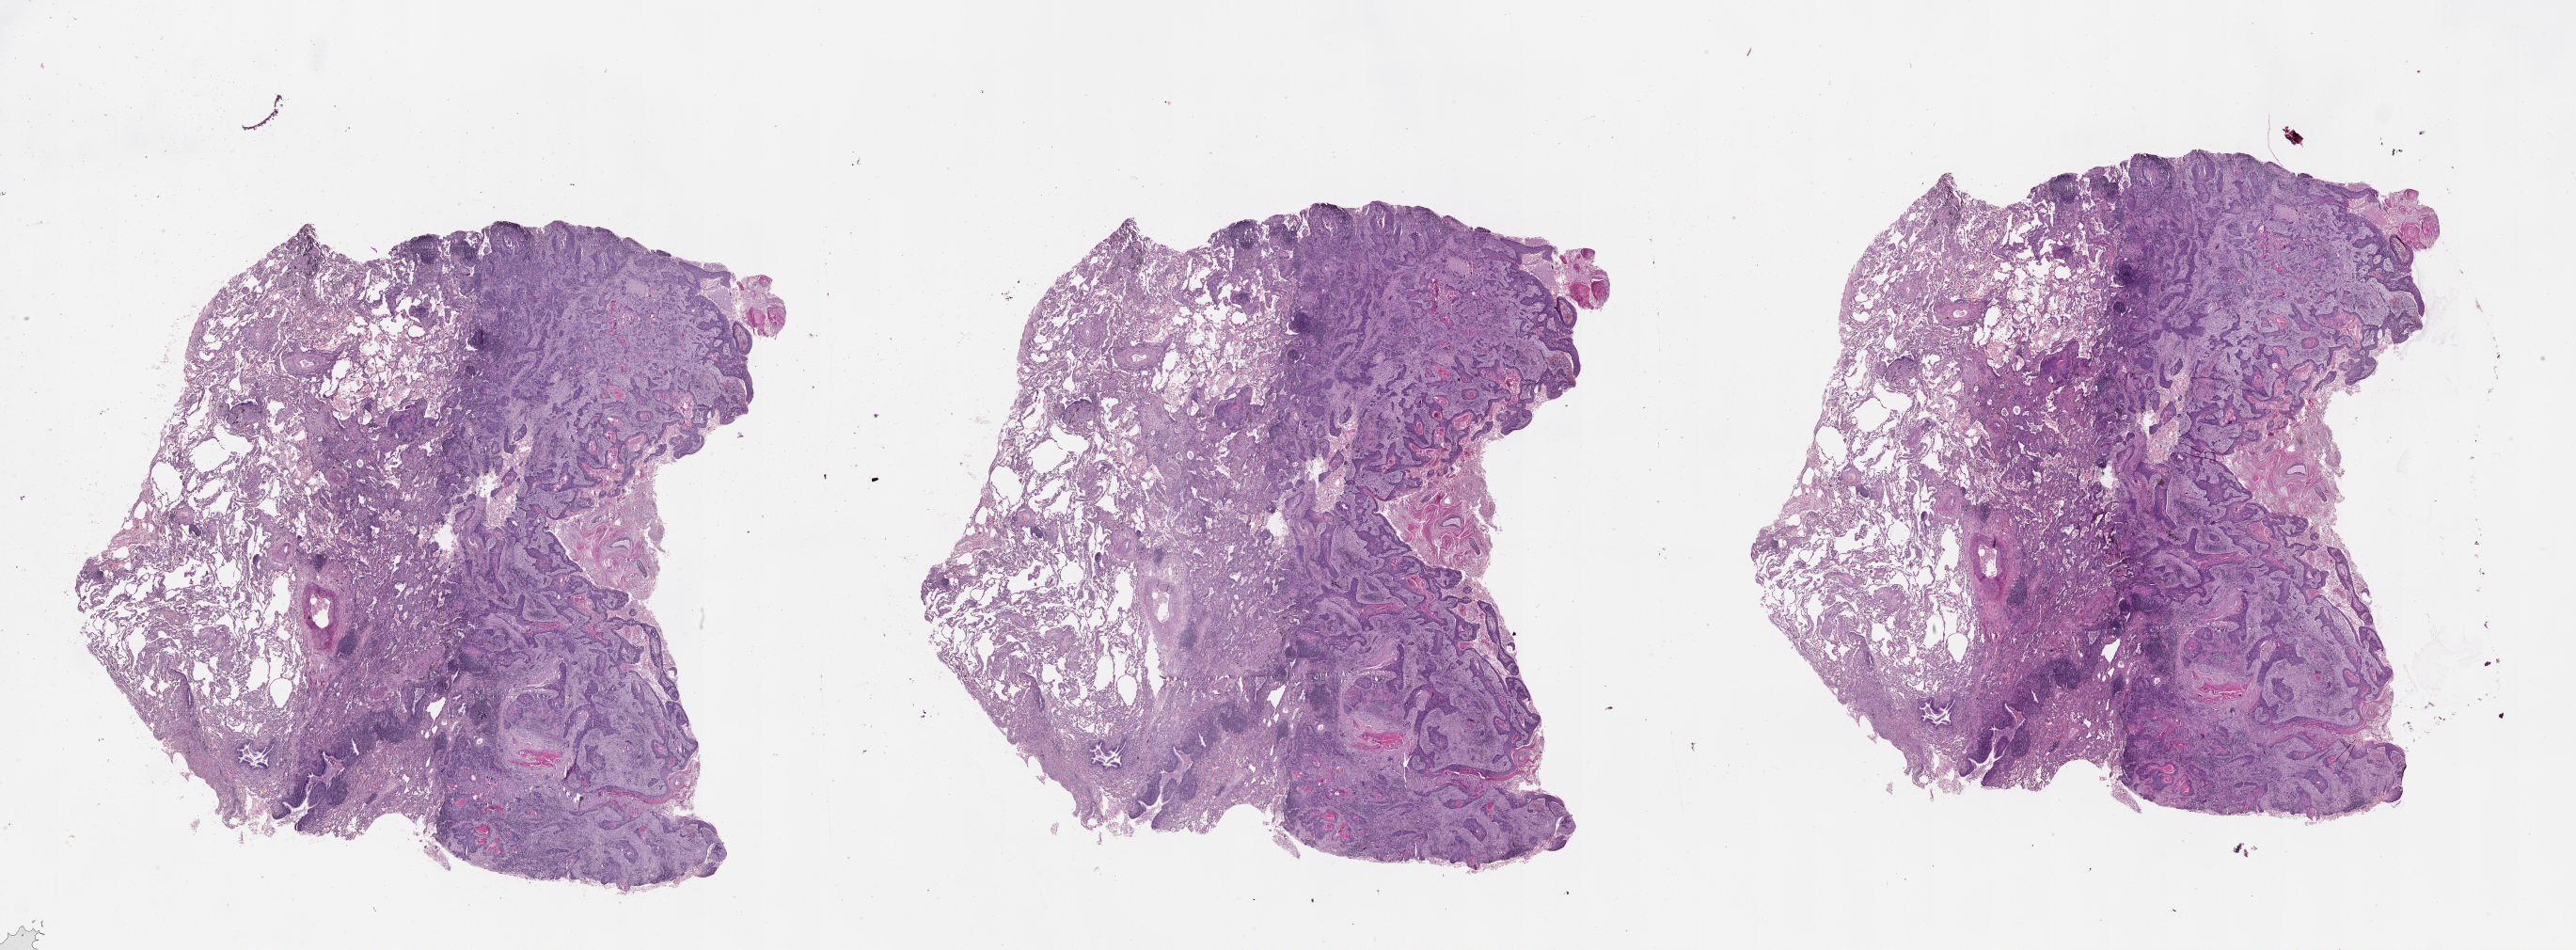
Digitized H&E-stained tissue section (whole slide), a low-resolution overview of the entire scanned area, about 44.1 x 16.3 mm (acquisition: 20x scan), lung, tumour tissue. Male, 72 y/o.
Patient diagnosis (cohort enrolment): squamous cell carcinoma (lung).